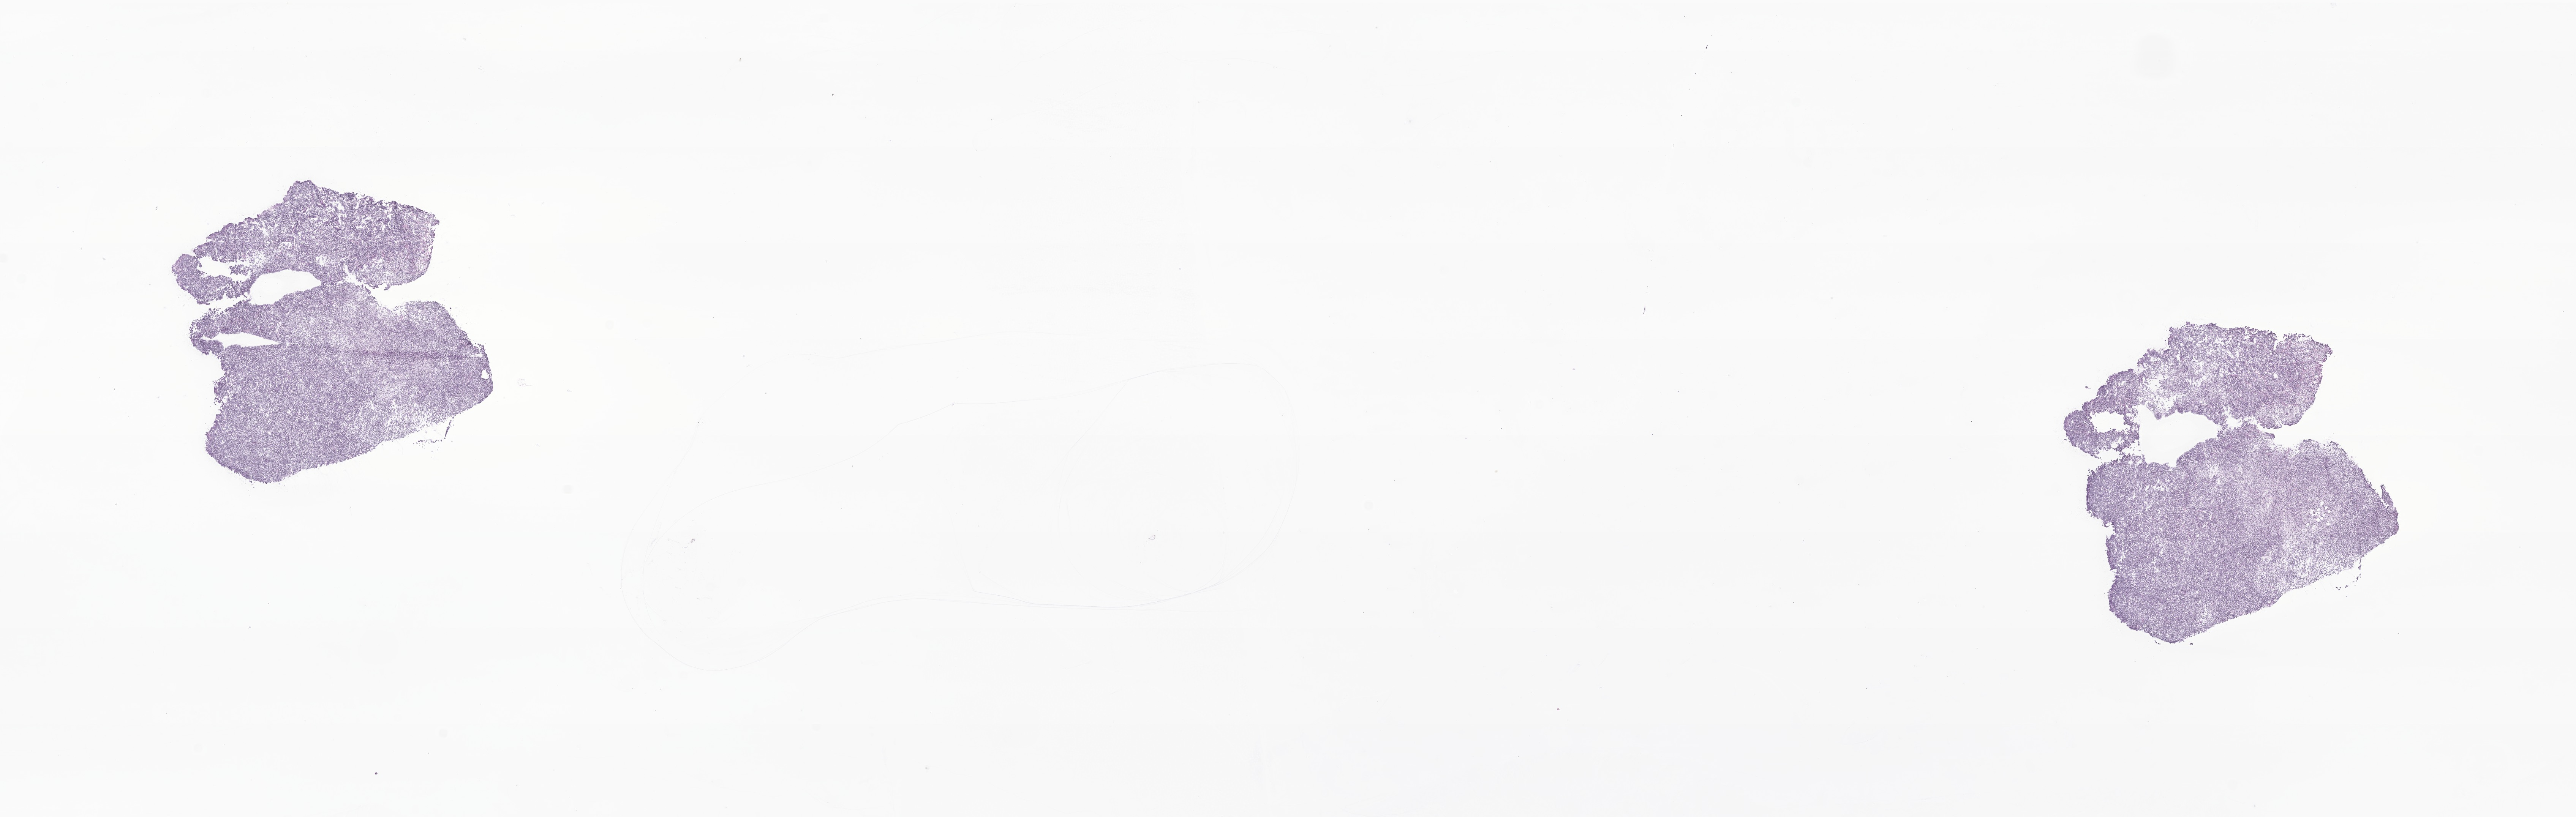
Haematoxylin and eosin whole-slide image of tumor tissue from the brain — low-resolution overview of the scanned area, about 28.6 x 9.1 mm. Cryosection (OCT / tissue freezing medium). Patient: male, age 209 months (17 years 5 months).
Diagnosis: Medulloblastoma, NOS.